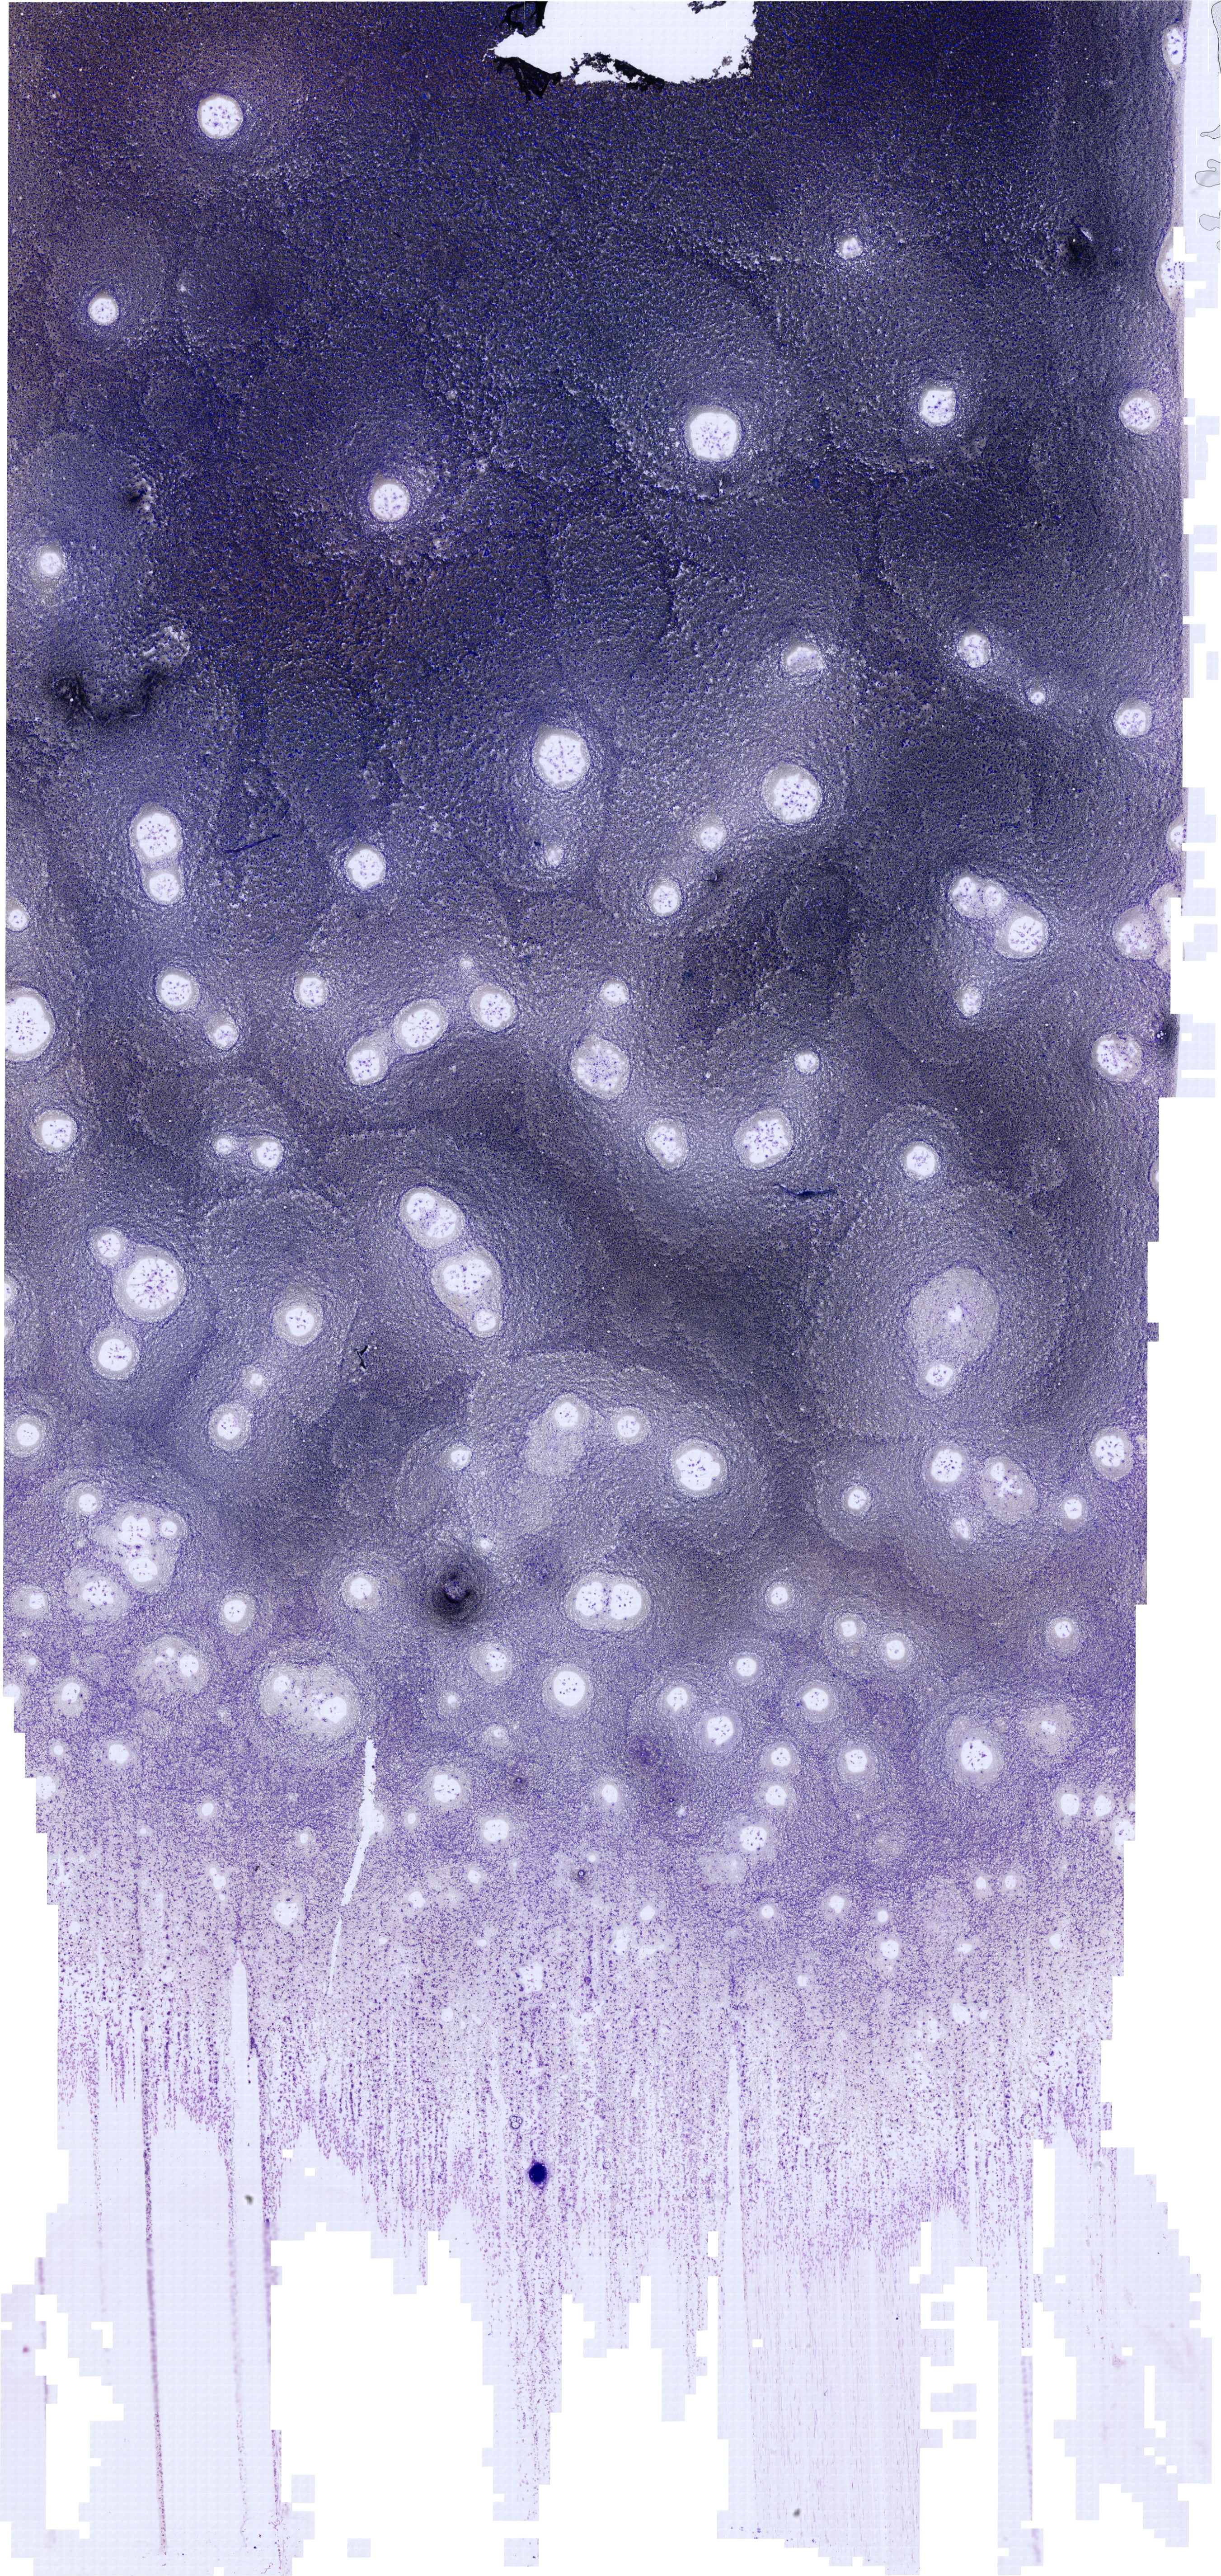
May-Grünwald–Giemsa-stained marrow aspirate smear (whole slide), whole scanned area (about 21.1 x 44.5 mm) shown as a low-resolution overview. Male patient.
Diagnosis: Burkitt Leukemia.